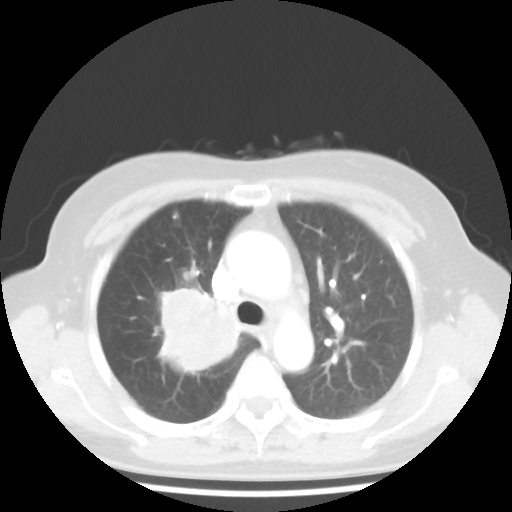
Chest CT, one axial slice. Slice 30 of 44 in the series (ordered by position). Reconstruction kernel STANDARD. 100 kVp. Lung window (W 1500 / L -600 HU). 512 × 512 image matrix, field of view 316 × 316 mm. Female patient, age 62 years. Case-level facts recorded for this patient, not image findings: clinical TNM (as recorded): T3 N0 M0; histopathological grade: G3.
Annotated regions visible in this slice (rectangle marked by the reading radiologist):
- lung tumour (recorded histology: small cell carcinoma): box from (x=143, y=272) to (x=251, y=375) px